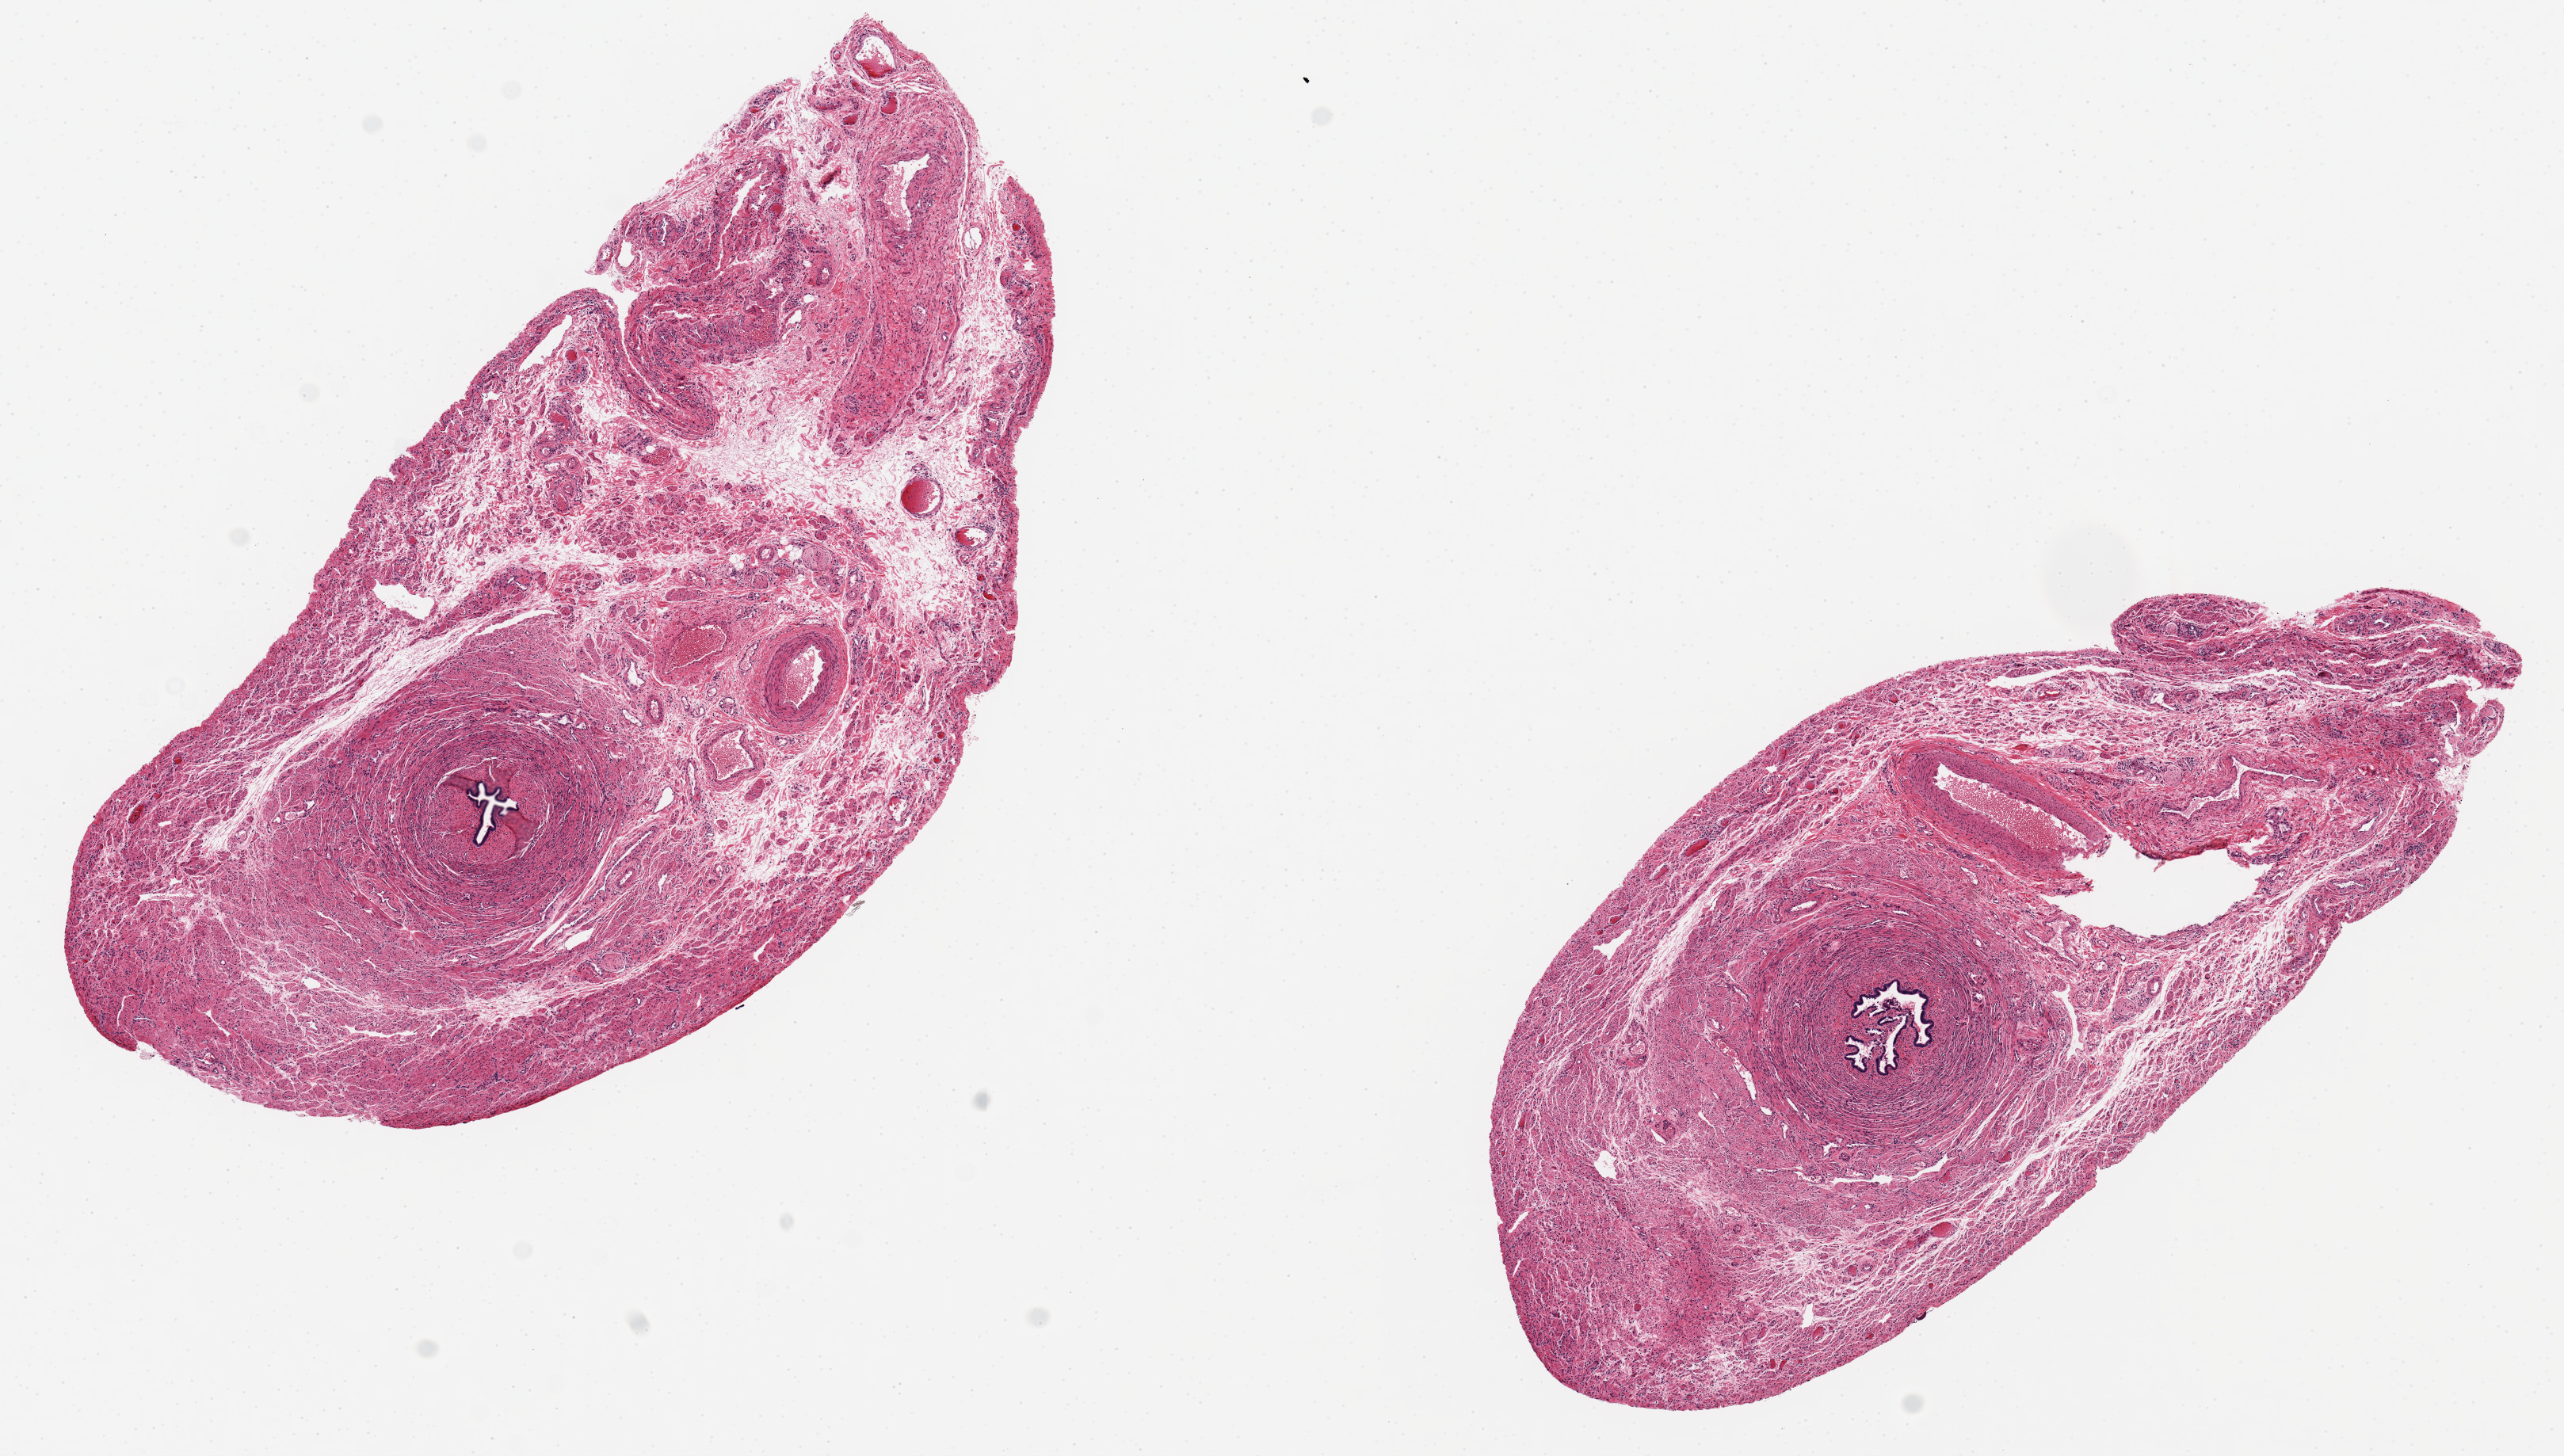
Digitized hematoxylin and eosin (H&E)-stained section — whole scanned area (about 12.8 x 7.3 mm, slide scanned at 20x) shown as a low-resolution overview; PAXgene-fixed paraffin-embedded (PFPE) section; section of fallopian tube (target tissue); donor tissue sample. Donor sex: female.
- pathologist's review note for this sample: 2 ~6x3mm aliquots. Lumen is ~0.4.x0.3mm in the center of each